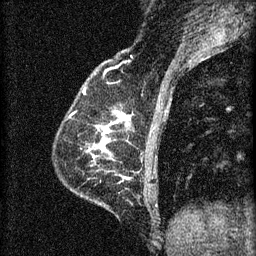
Breast MRI (dynamic contrast-enhanced), one sagittal slice. Slice 20 of 60 in the series (ordered by position). 3 images stored at this slice position (order not interpretable as contrast timing). 1.5 T. TE 4.2 ms, TR 8.2 ms. 2 mm slice thickness. 256 × 256 image matrix, field of view 180 × 180 mm. Female patient, age 59 years.
Outlined on this slice (semi-automatic segmentation, software-assisted and operator-edited):
- analysis volume of interest (the breast-tissue region the enhancement analysis was run in; not a lesion): bounding box <66,104,134,161> (left, top, right, bottom; pixels)
- tumour enhancement mask (voxels above the 70 % enhancement threshold inside the analysis volume of interest): <99,114,128,129>